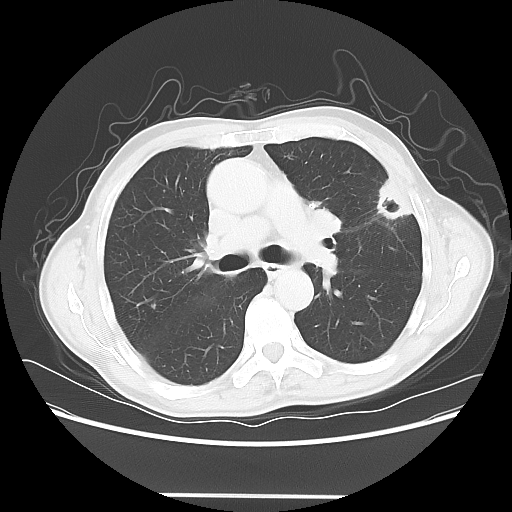
Chest CT, one axial slice; reconstruction kernel LUNG; 120 kVp; lung window (W 1500 / L -600 HU); 512 × 512 image matrix. Male patient, age 71 years. Case-level facts recorded for this patient, not image findings: clinical TNM (as recorded): T1c N0 M0; histopathological grade: G2-3.
Structures marked on this image (rectangle marked by the reading radiologist):
- lung tumour (recorded histology: adenocarcinoma): bounding box <368,177,415,225> (left, top, right, bottom; pixels)